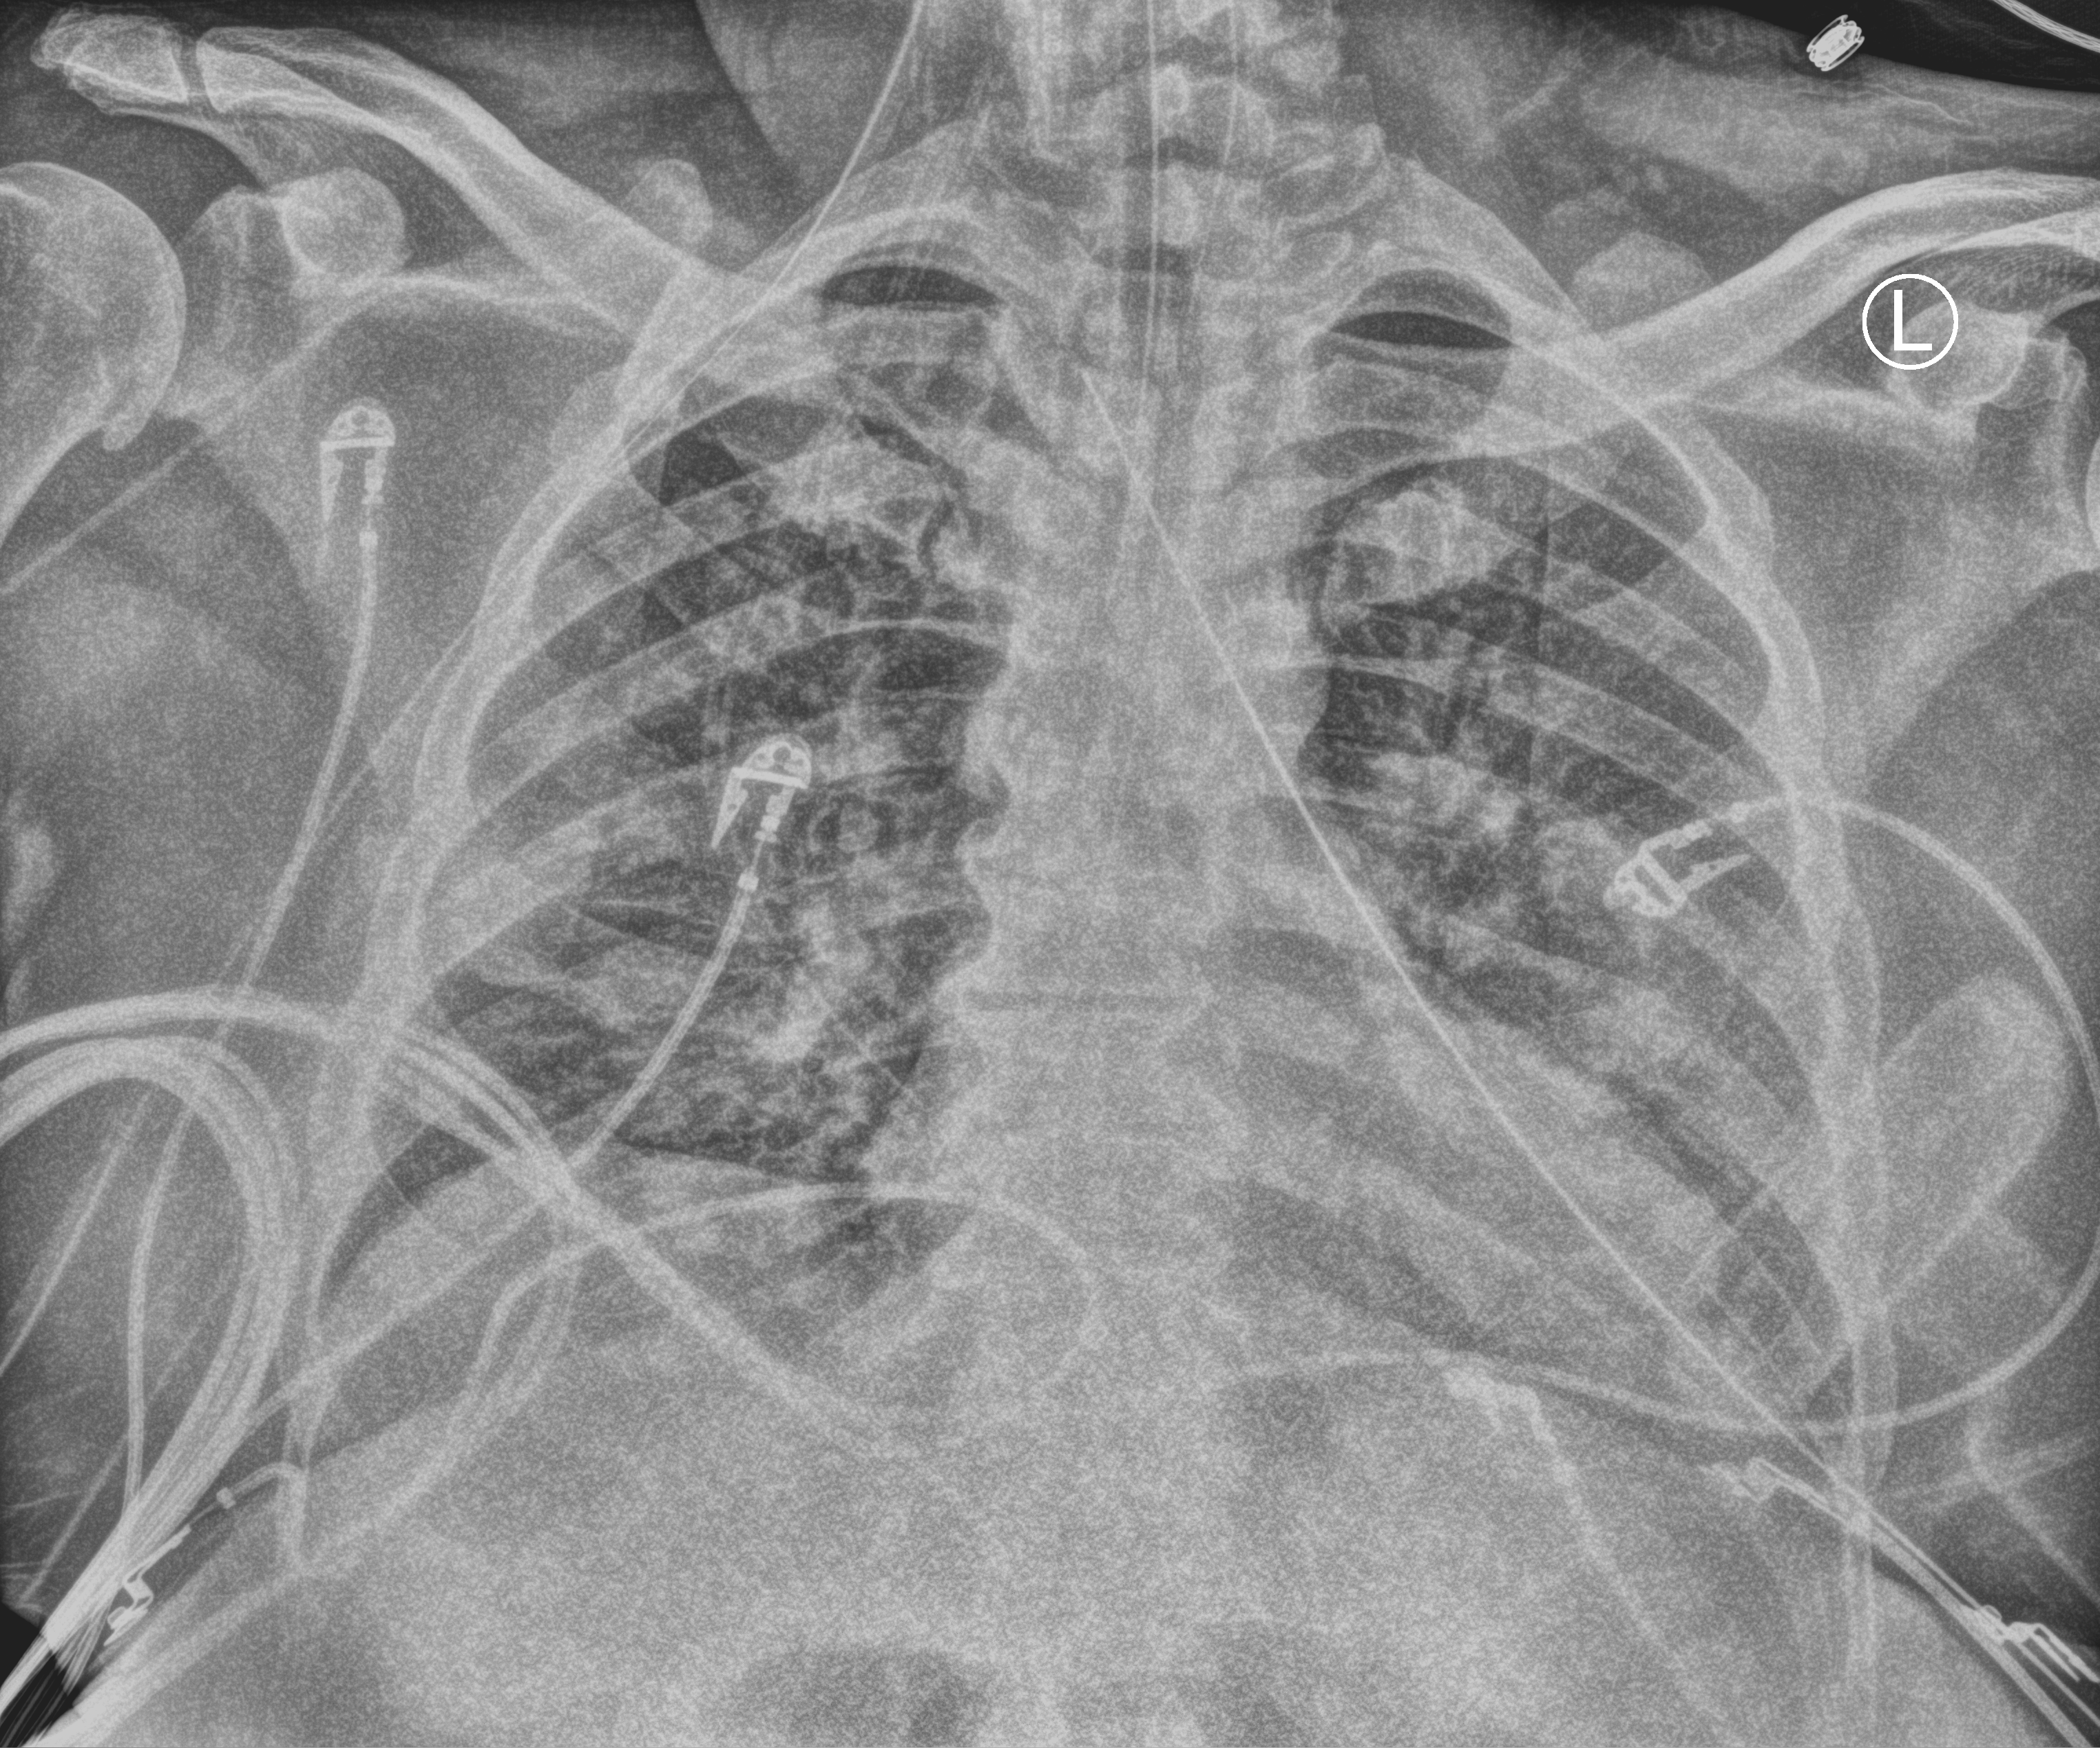
Chest X-ray (portable). Patient hospitalised with COVID-19; male, aged 18–59 years.
From the hospital-stay record, not from the radiograph (when in the stay this image was taken is not recorded): admitted to intensive care during this hospital stay: yes.